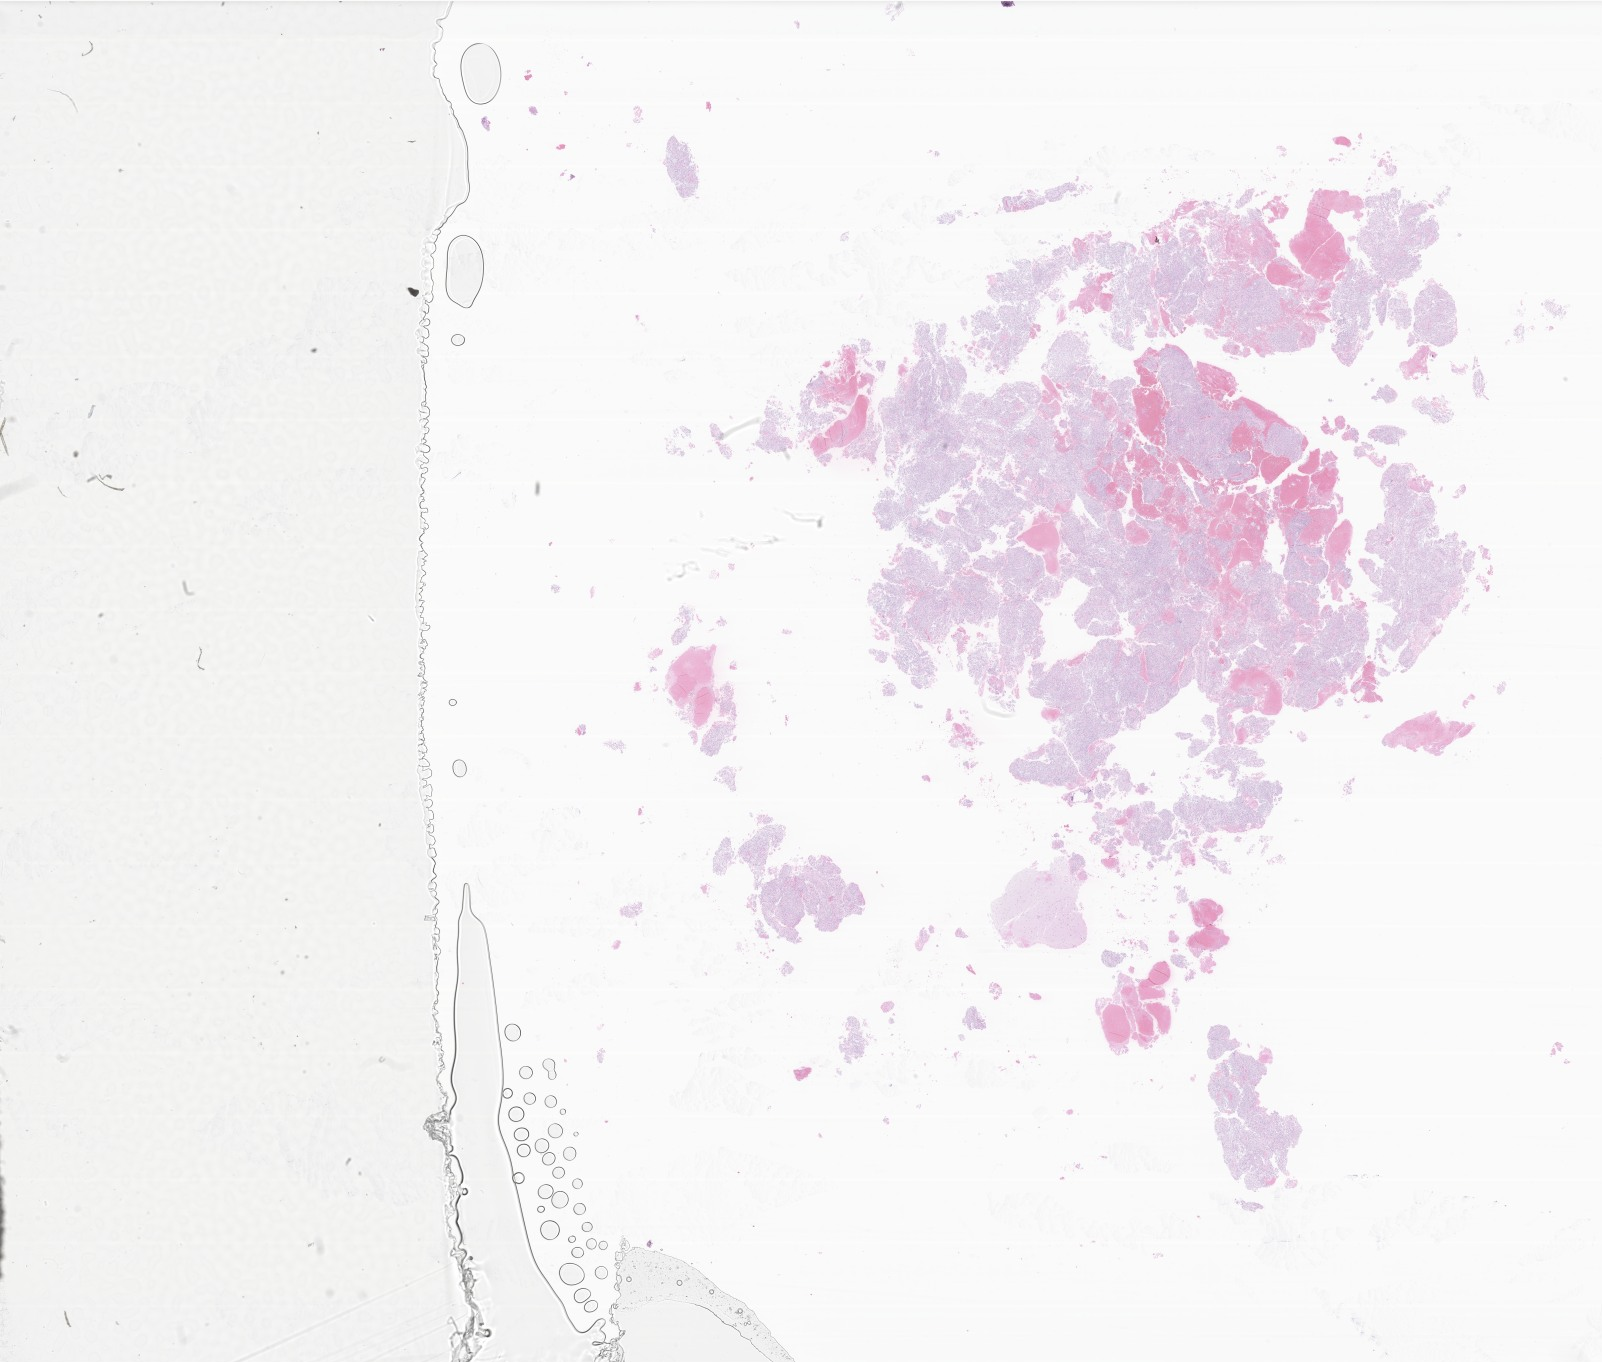
Whole-slide image, hematoxylin and eosin (H&E) stain of tumor tissue from the brain, low-resolution overview of the scanned area, about 27.0 x 23.0 mm. FFPE section. Patient female; age 780 days (about 2.1 years).
- diagnosis: Neoplasm, uncertain whether benign or malignant